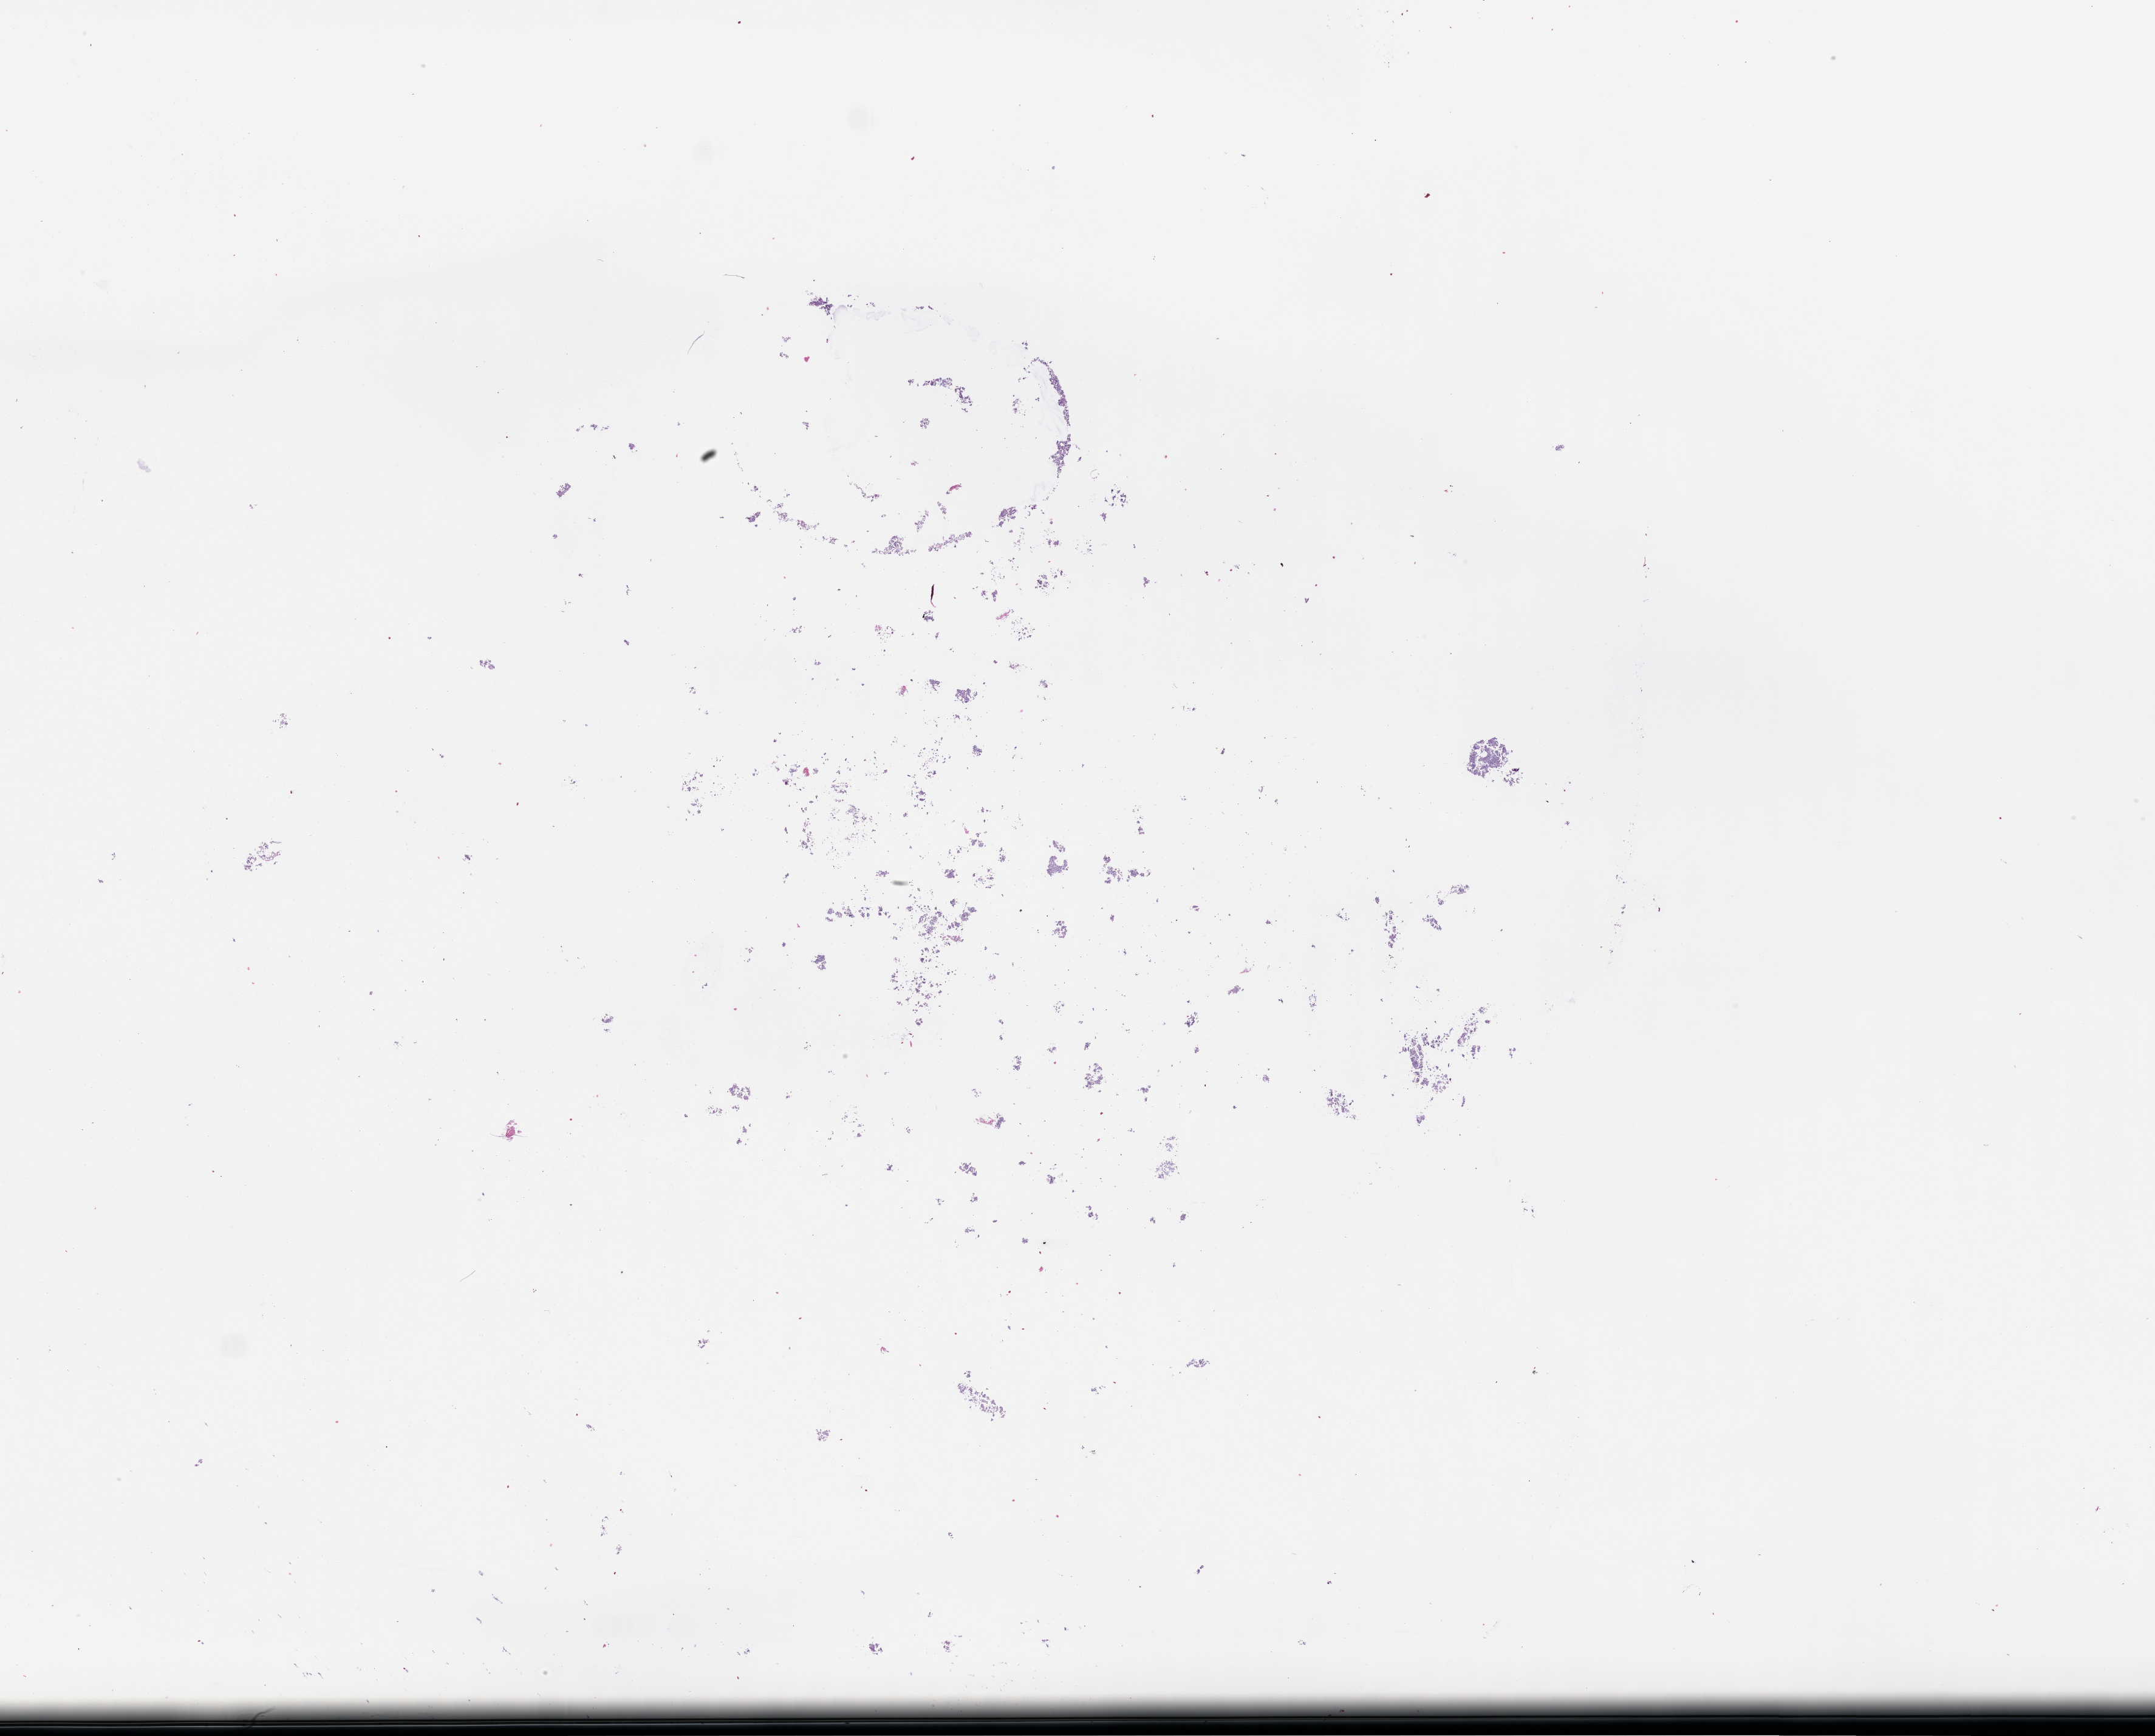
Digitized H&E-stained section — whole scanned area (about 28.6 x 23.1 mm) shown as a low-resolution overview, formalin-fixed paraffin-embedded section, tissue site: lung, specimen time point: archival tissue. Male patient.
This section: primary tumor. Diagnosis: Non-Small Cell Lung Carcinoma.